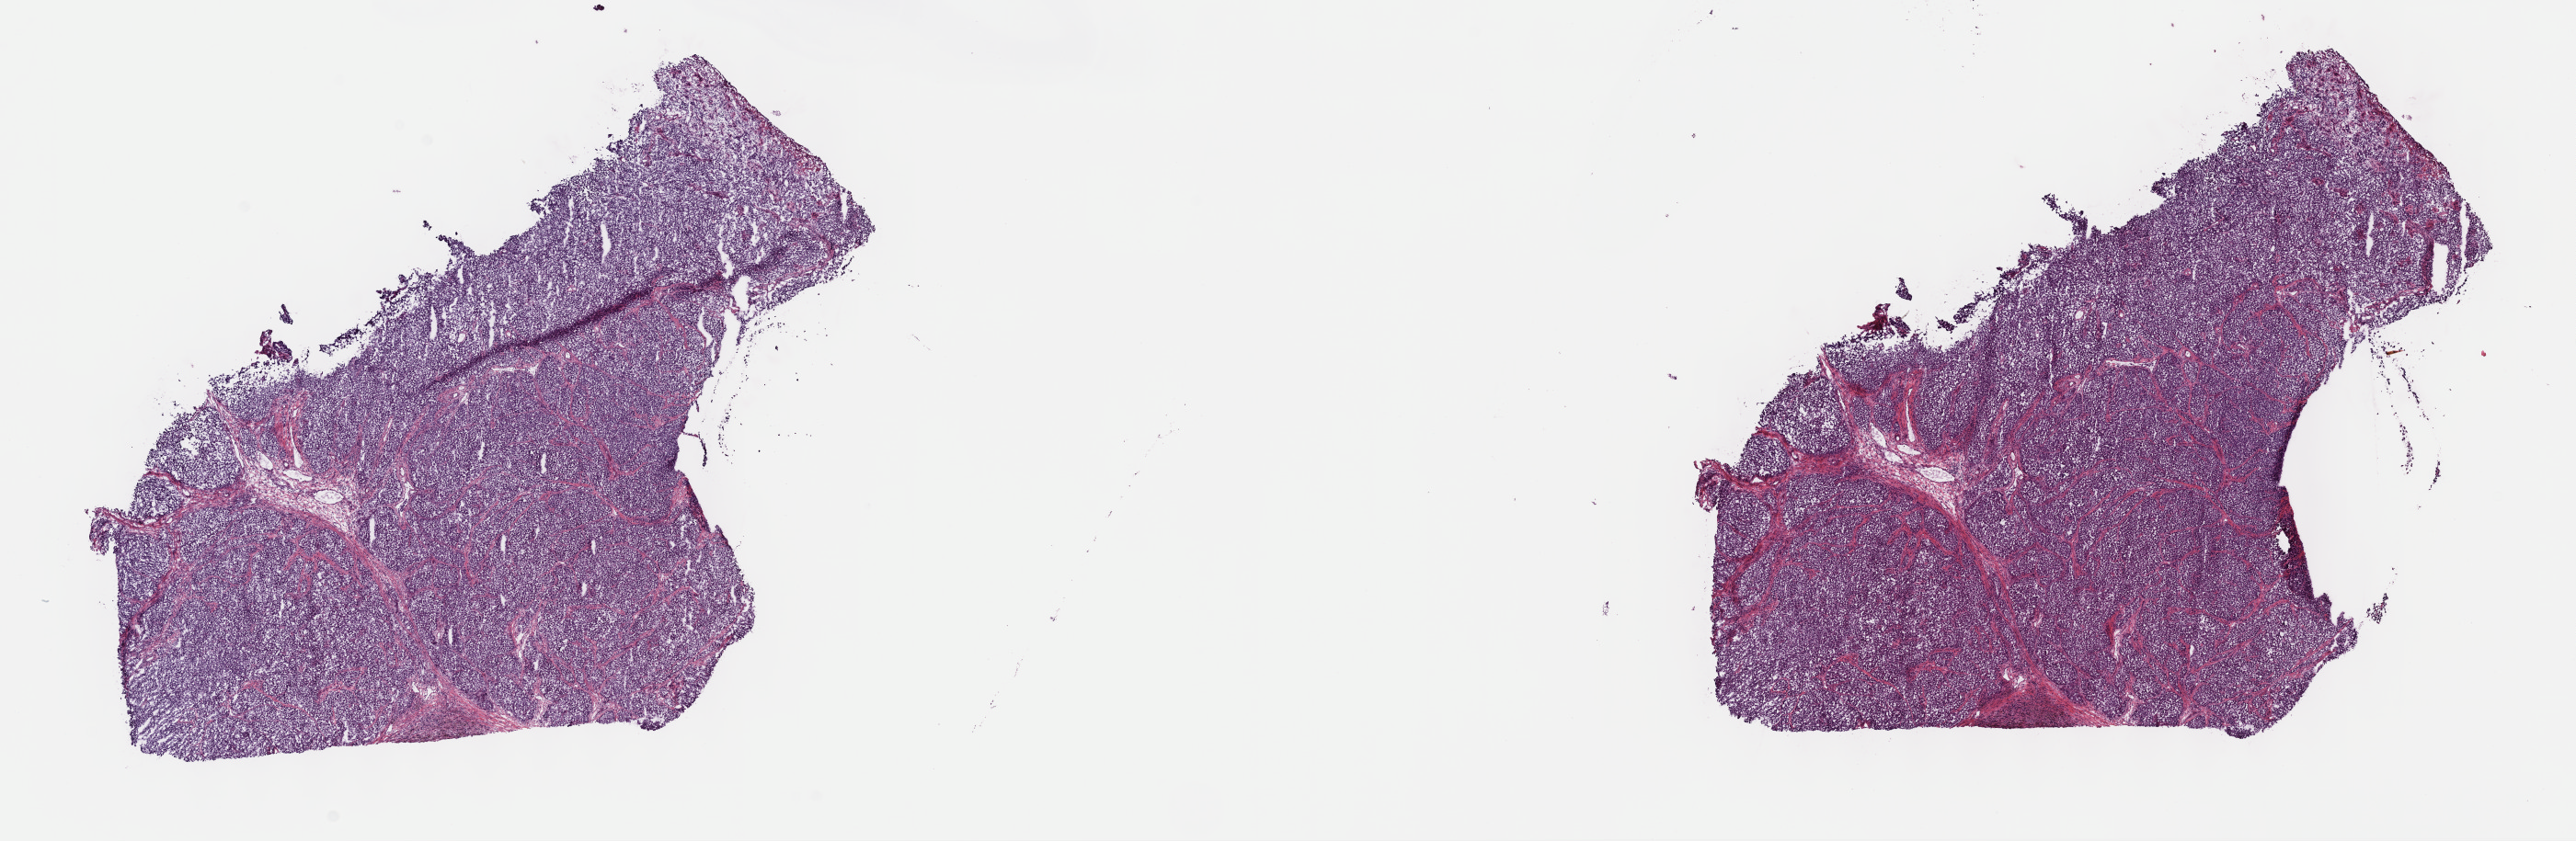
Whole-slide histology image, H&E-stained — a low-resolution overview of the entire scanned area, about 22.7 x 7.4 mm (acquisition: 40x scan); frozen section from the top of the tissue portion; primary tumour sample from the skin. Patient: male, age at initial diagnosis 86 years. Composition of this section per pathologist review: tumour cells 100%, tumour nuclei 75%.
Histologic diagnosis: Epithelioid cell melanoma.